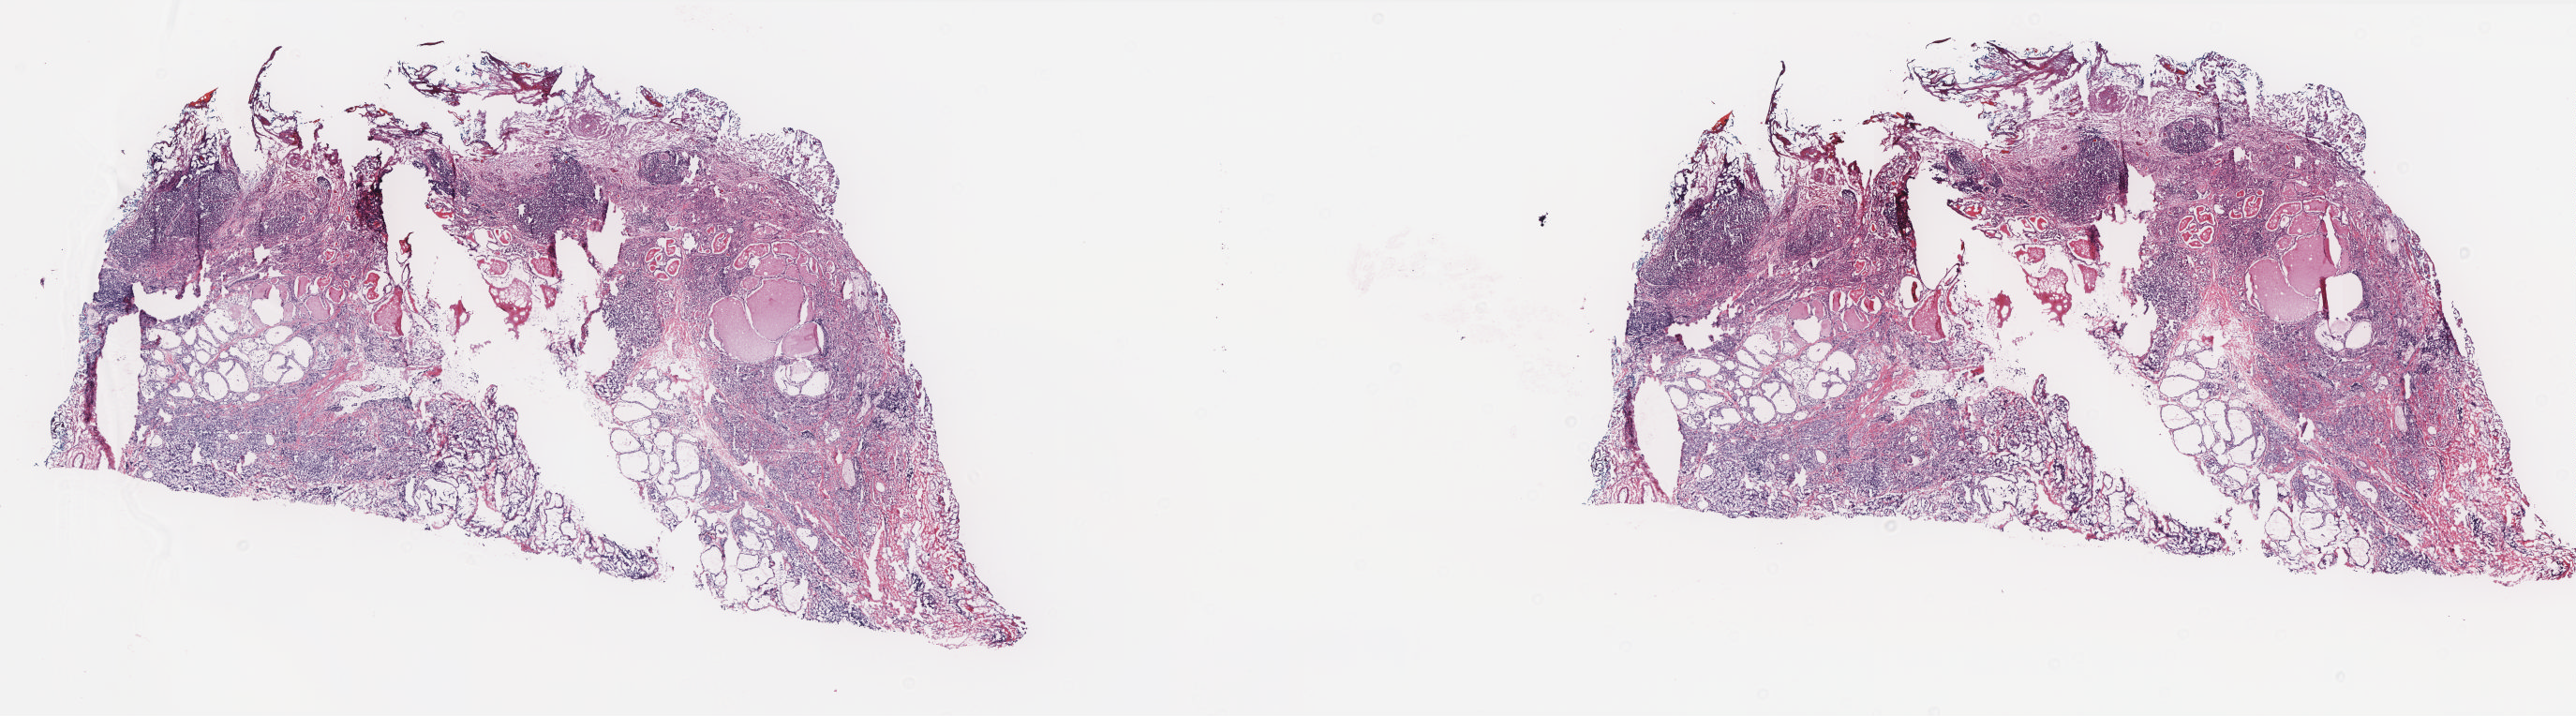
H&E whole-slide image, shown as a low-resolution overview of the whole scanned area (about 22.0 x 6.1 mm, slide scanned at 20x). Frozen section. Thyroid, solid tissue normal (non-tumour tissue) sample. Female patient; age at initial diagnosis 18 years.
This section: solid tissue normal sample (biorepository sample class). Patient diagnosis: Papillary adenocarcinoma, NOS.